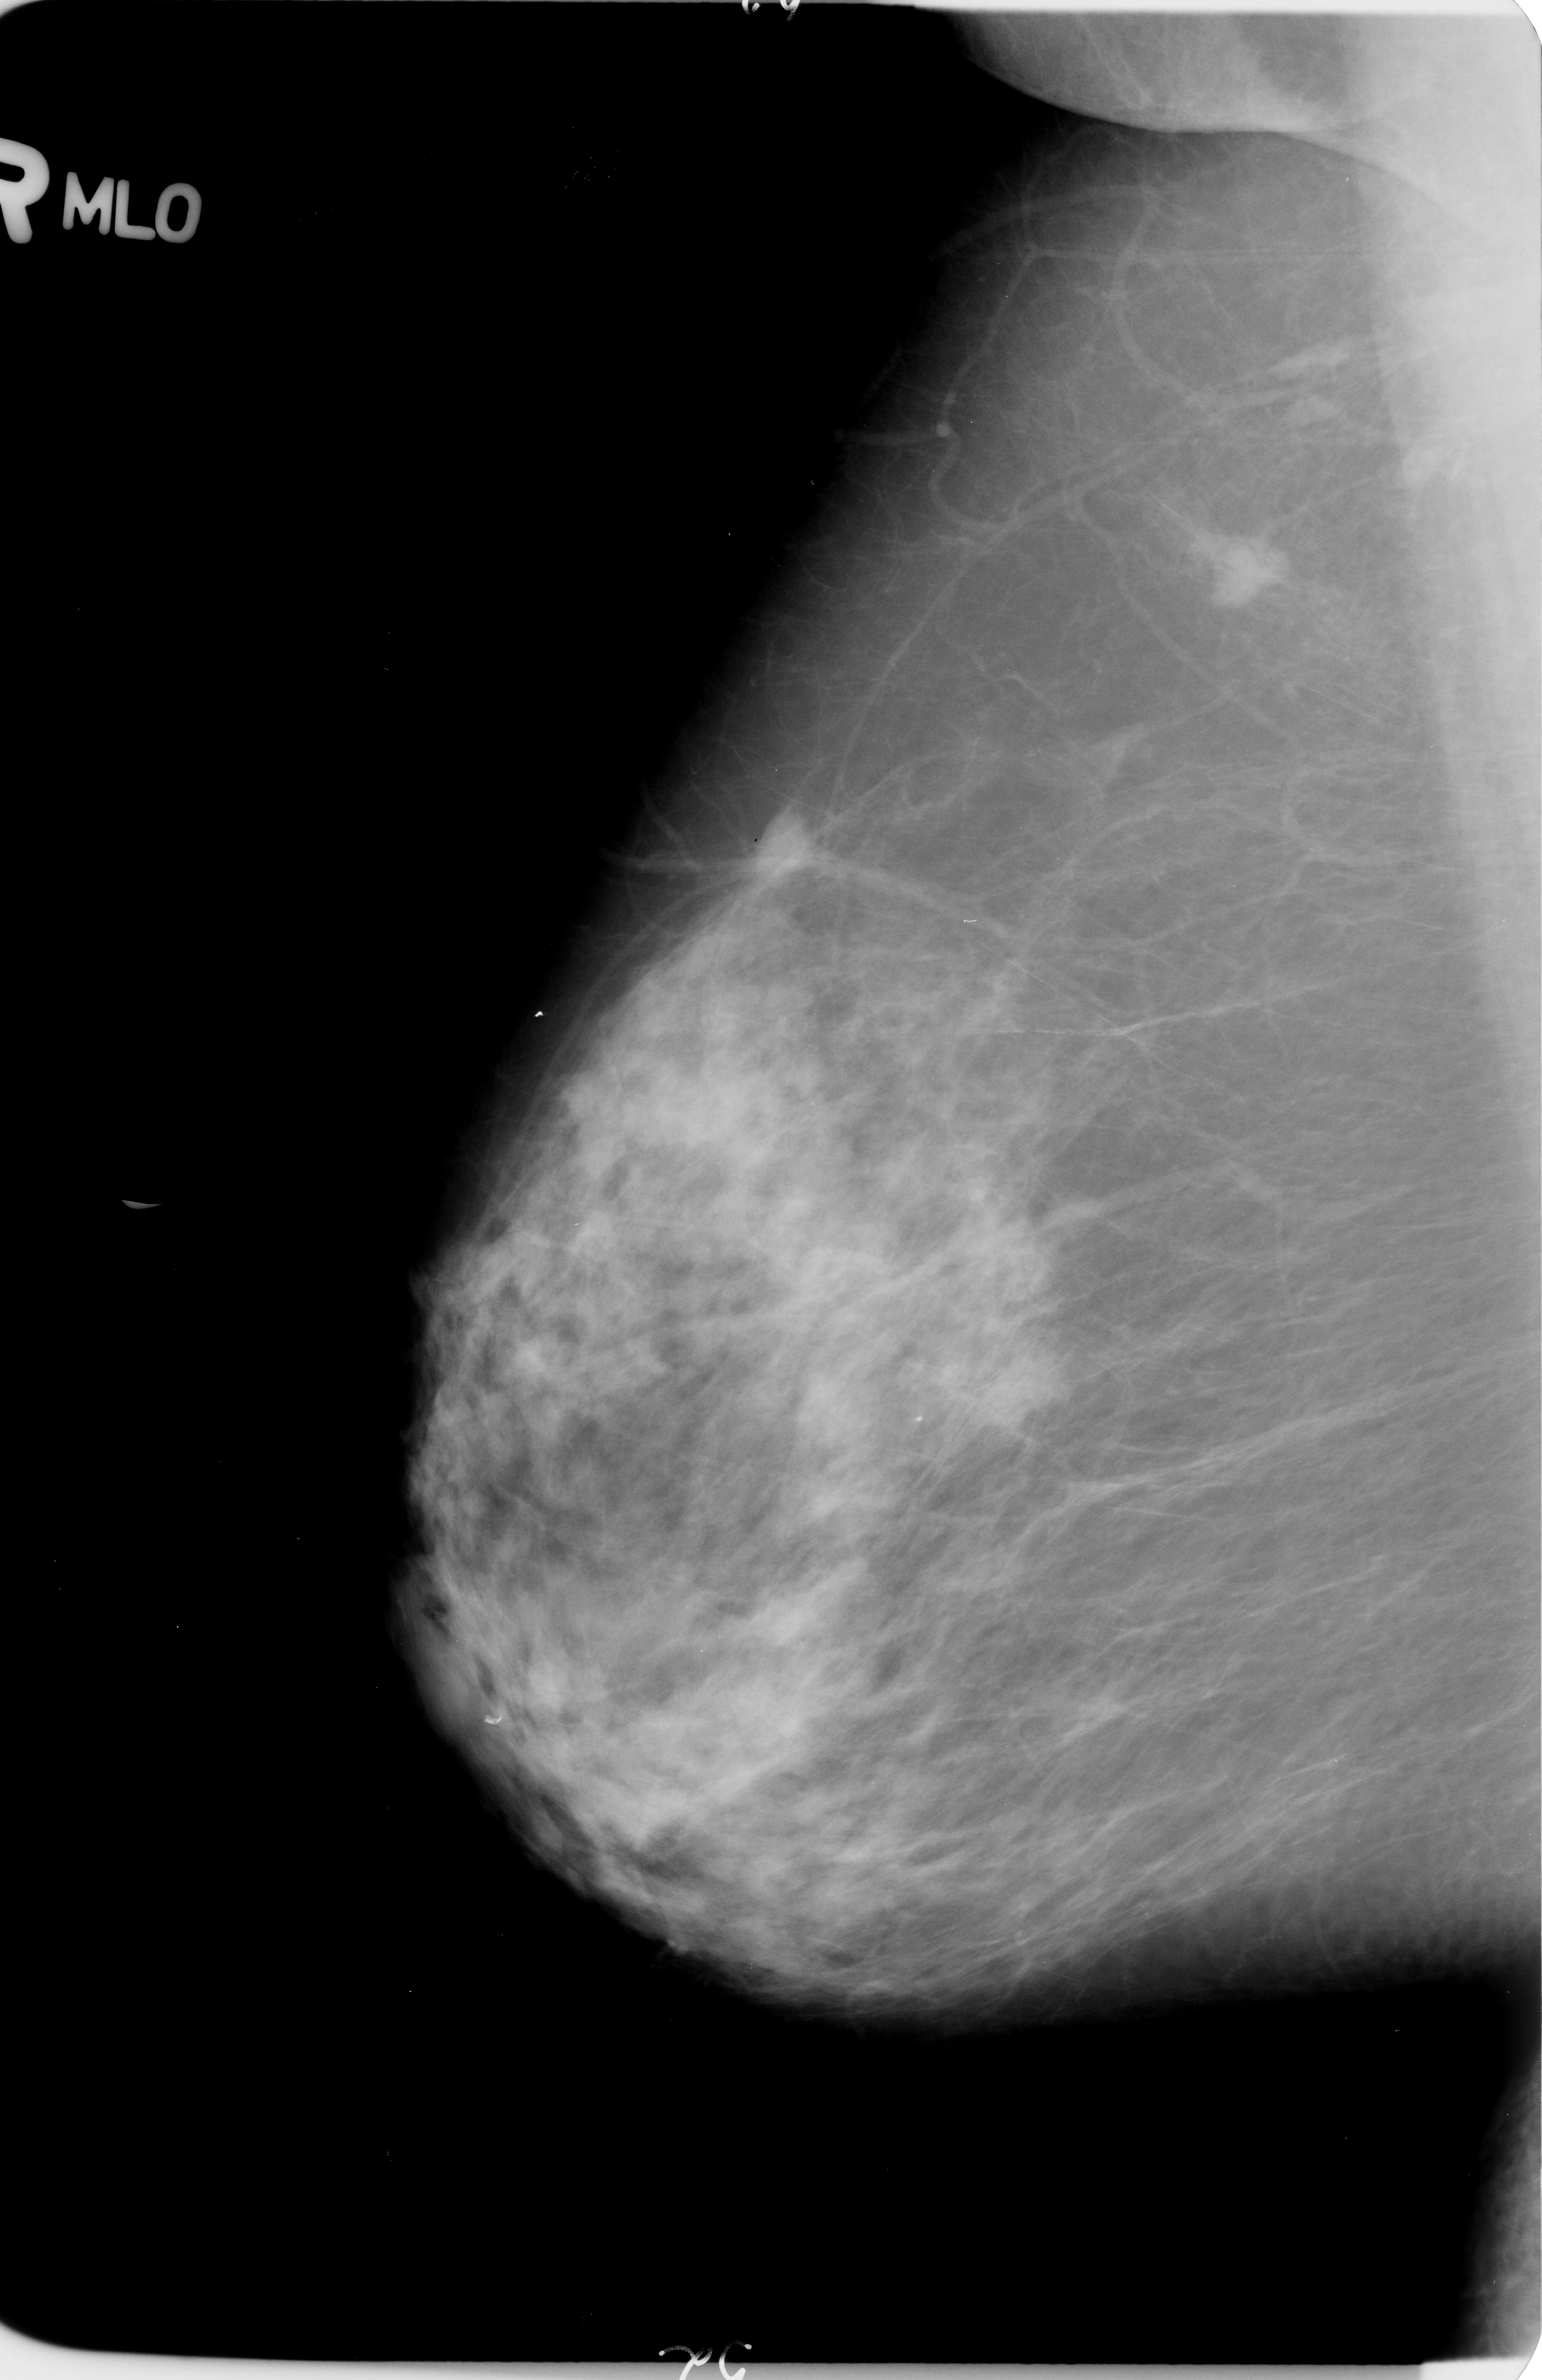
Scanned film-screen mammogram, right breast, mediolateral oblique (MLO) view, BI-RADS breast density category 3 (scale 1–4).
Mass, shape irregular, margins spiculated; BI-RADS assessment category 4; subtlety rating 3 on a 1 (subtle) to 5 (obvious) scale; pathology result (as recorded, not read from the image): malignant.